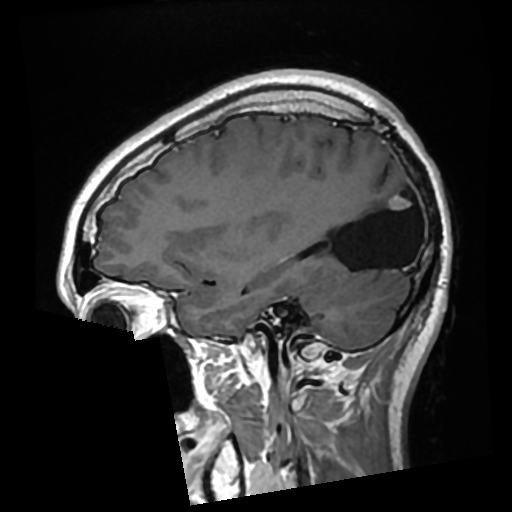
Brain MRI from a brain-tumour surgery series, one sagittal slice; position 94 of 276 along the scan axis; T1-weighted post-contrast; 0.7 mm slice thickness; 512 × 512 image matrix. Case-level facts recorded for this patient, not image findings: histopathology: Glioma with ependymal features; WHO grade: 2; tumour location: Left Parietal.
Structures marked on this image (manually delineated by an expert):
- previous resection cavity: bounding box <327,182,415,270> (left, top, right, bottom; pixels)
- tumour: <390,196,411,211>